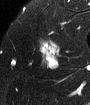
MRI of an extremity soft-tissue mass, one axial slice. Position 49 of 65 along the scan axis. T2-weighted fat-saturated. MR volume resampled by the dataset authors to the PET/CT grid (not the native acquisition matrix). 90 × 105 image matrix. Male patient. From the clinical record (not read from this slice): histological type: mixoid liposarcoma; grade: low; site of the primary tumour: left thigh.
Annotated regions visible in this slice (expert contour drawn on MRI and transferred to this co-registered scan by the dataset authors):
- gross tumour volume (mass): box from (x=39, y=43) to (x=56, y=56) px